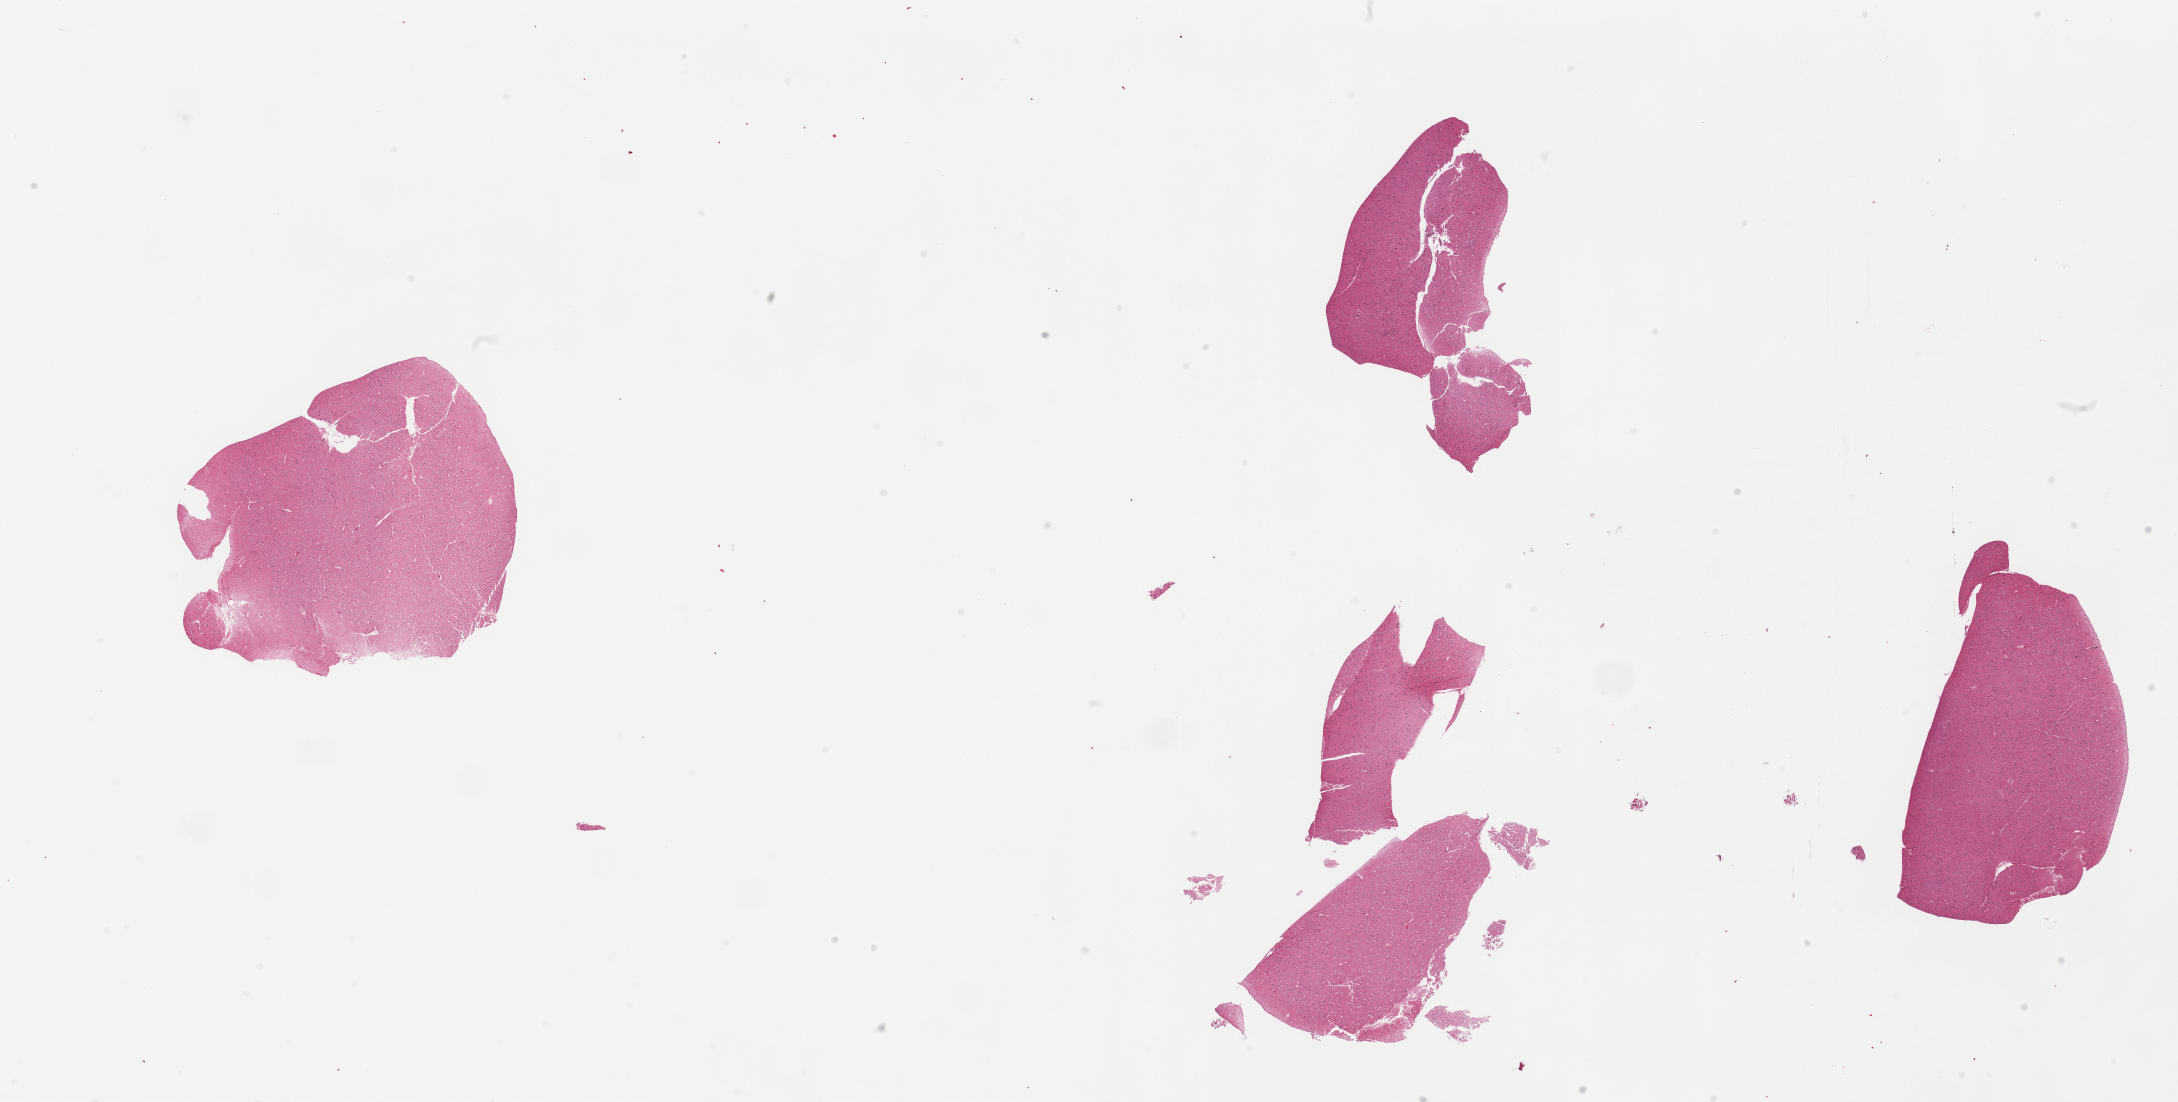
Hematoxylin and eosin (H&E) whole-slide image, brightfield, whole scanned area (about 34.5 x 17.4 mm) shown as a low-resolution overview; PAXgene-fixed, paraffin-embedded tissue; section of cerebral cortex (target tissue); donor tissue sample. Donor: male.
* reviewer comment on this tissue sample: 4 pieces